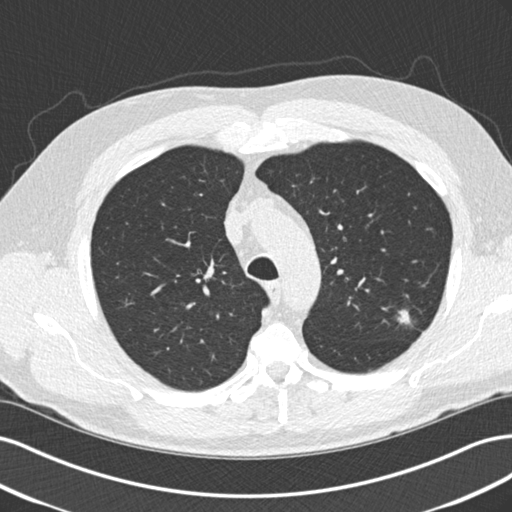
Low-dose screening chest CT, one axial slice. Reconstruction kernel B30f. 120 kVp. Lung window (W 1500 / L -600 HU). 512 × 512 image matrix.
Annotated regions visible in this slice (manually delineated by an expert):
- lesion 1 (tumor, upper lobe of left lung): bounding box <398,310,411,324> (left, top, right, bottom; pixels)